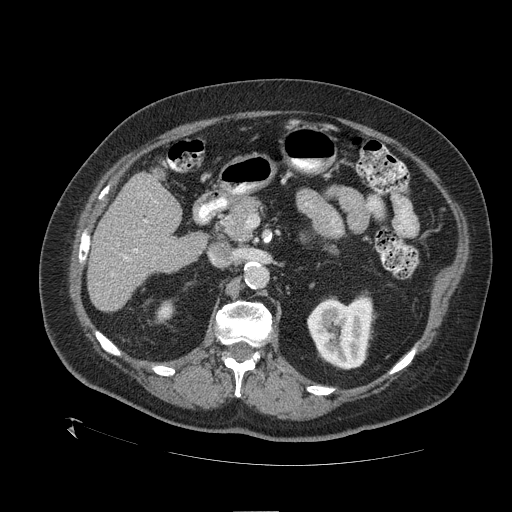
Contrast-enhanced abdominal CT (liver protocol), one axial slice. Position 57 of 109 along the scan axis. 120 kVp. One of 2 acquisitions stored at this slice position. Soft-tissue window (W 400 / L 40 HU). 512 × 512 image matrix, field of view 460 × 460 mm. Case-level facts recorded for this patient, not image findings: diagnosis: hepatocellular carcinoma (patient treated with transarterial chemoembolisation; whether this scan precedes or follows treatment is not stated here); TNM stage (as recorded): Stage-I; Child-Pugh class: A; tumour differentiation: no biopsy; tumour size: 4.6 cm.
Structures marked on this image (semi-automatically segmented with operator editing):
- liver parenchyma outside the tumour (the mass and vessels are separate outlines, so this box may not span the whole liver): bounding box [x1, y1, x2, y2] px = [88, 174, 206, 310]
- liver vessels: [124, 220, 147, 260]